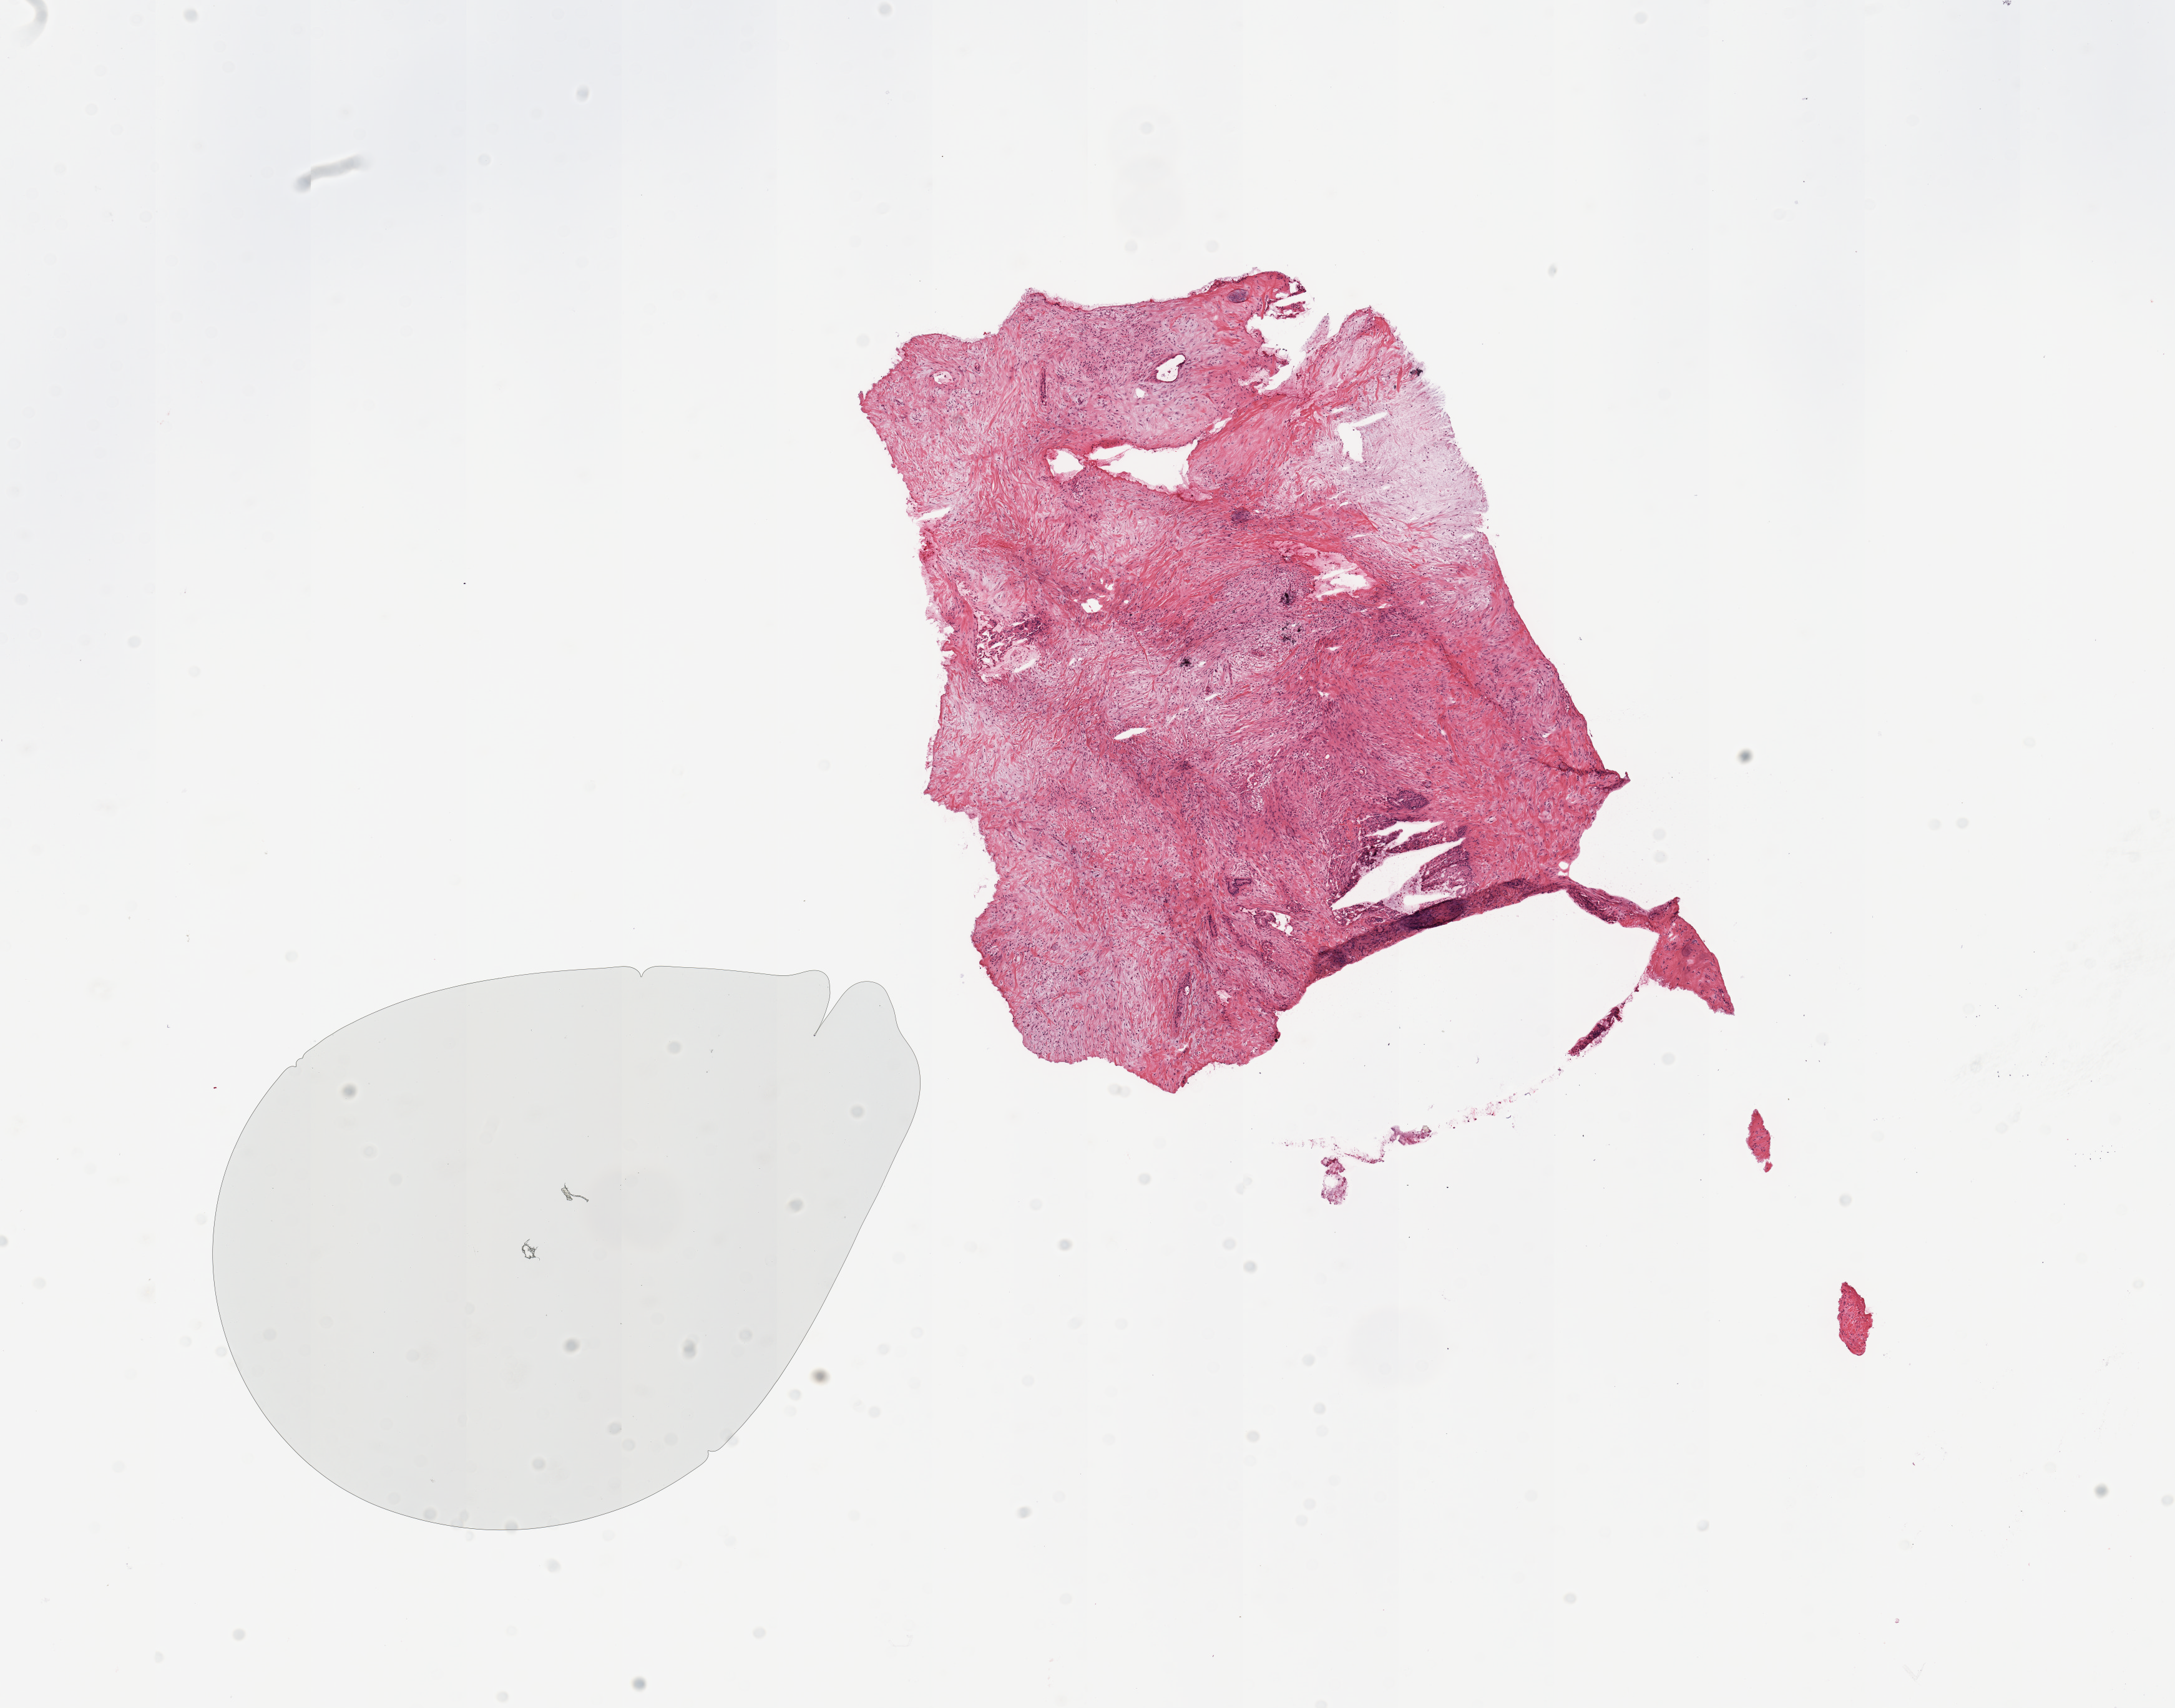
Hematoxylin and eosin (H&E) stained whole-slide image — whole scanned area (about 13.8 x 10.8 mm, slide scanned at 20x) shown as a low-resolution overview; pancreas, normal (non-tumour) tissue. Patient: male, age 75 years.
This section: normal (non-tumour) tissue from the same patient. Patient diagnosis (cohort enrolment): ductal adenocarcinoma (pancreas).